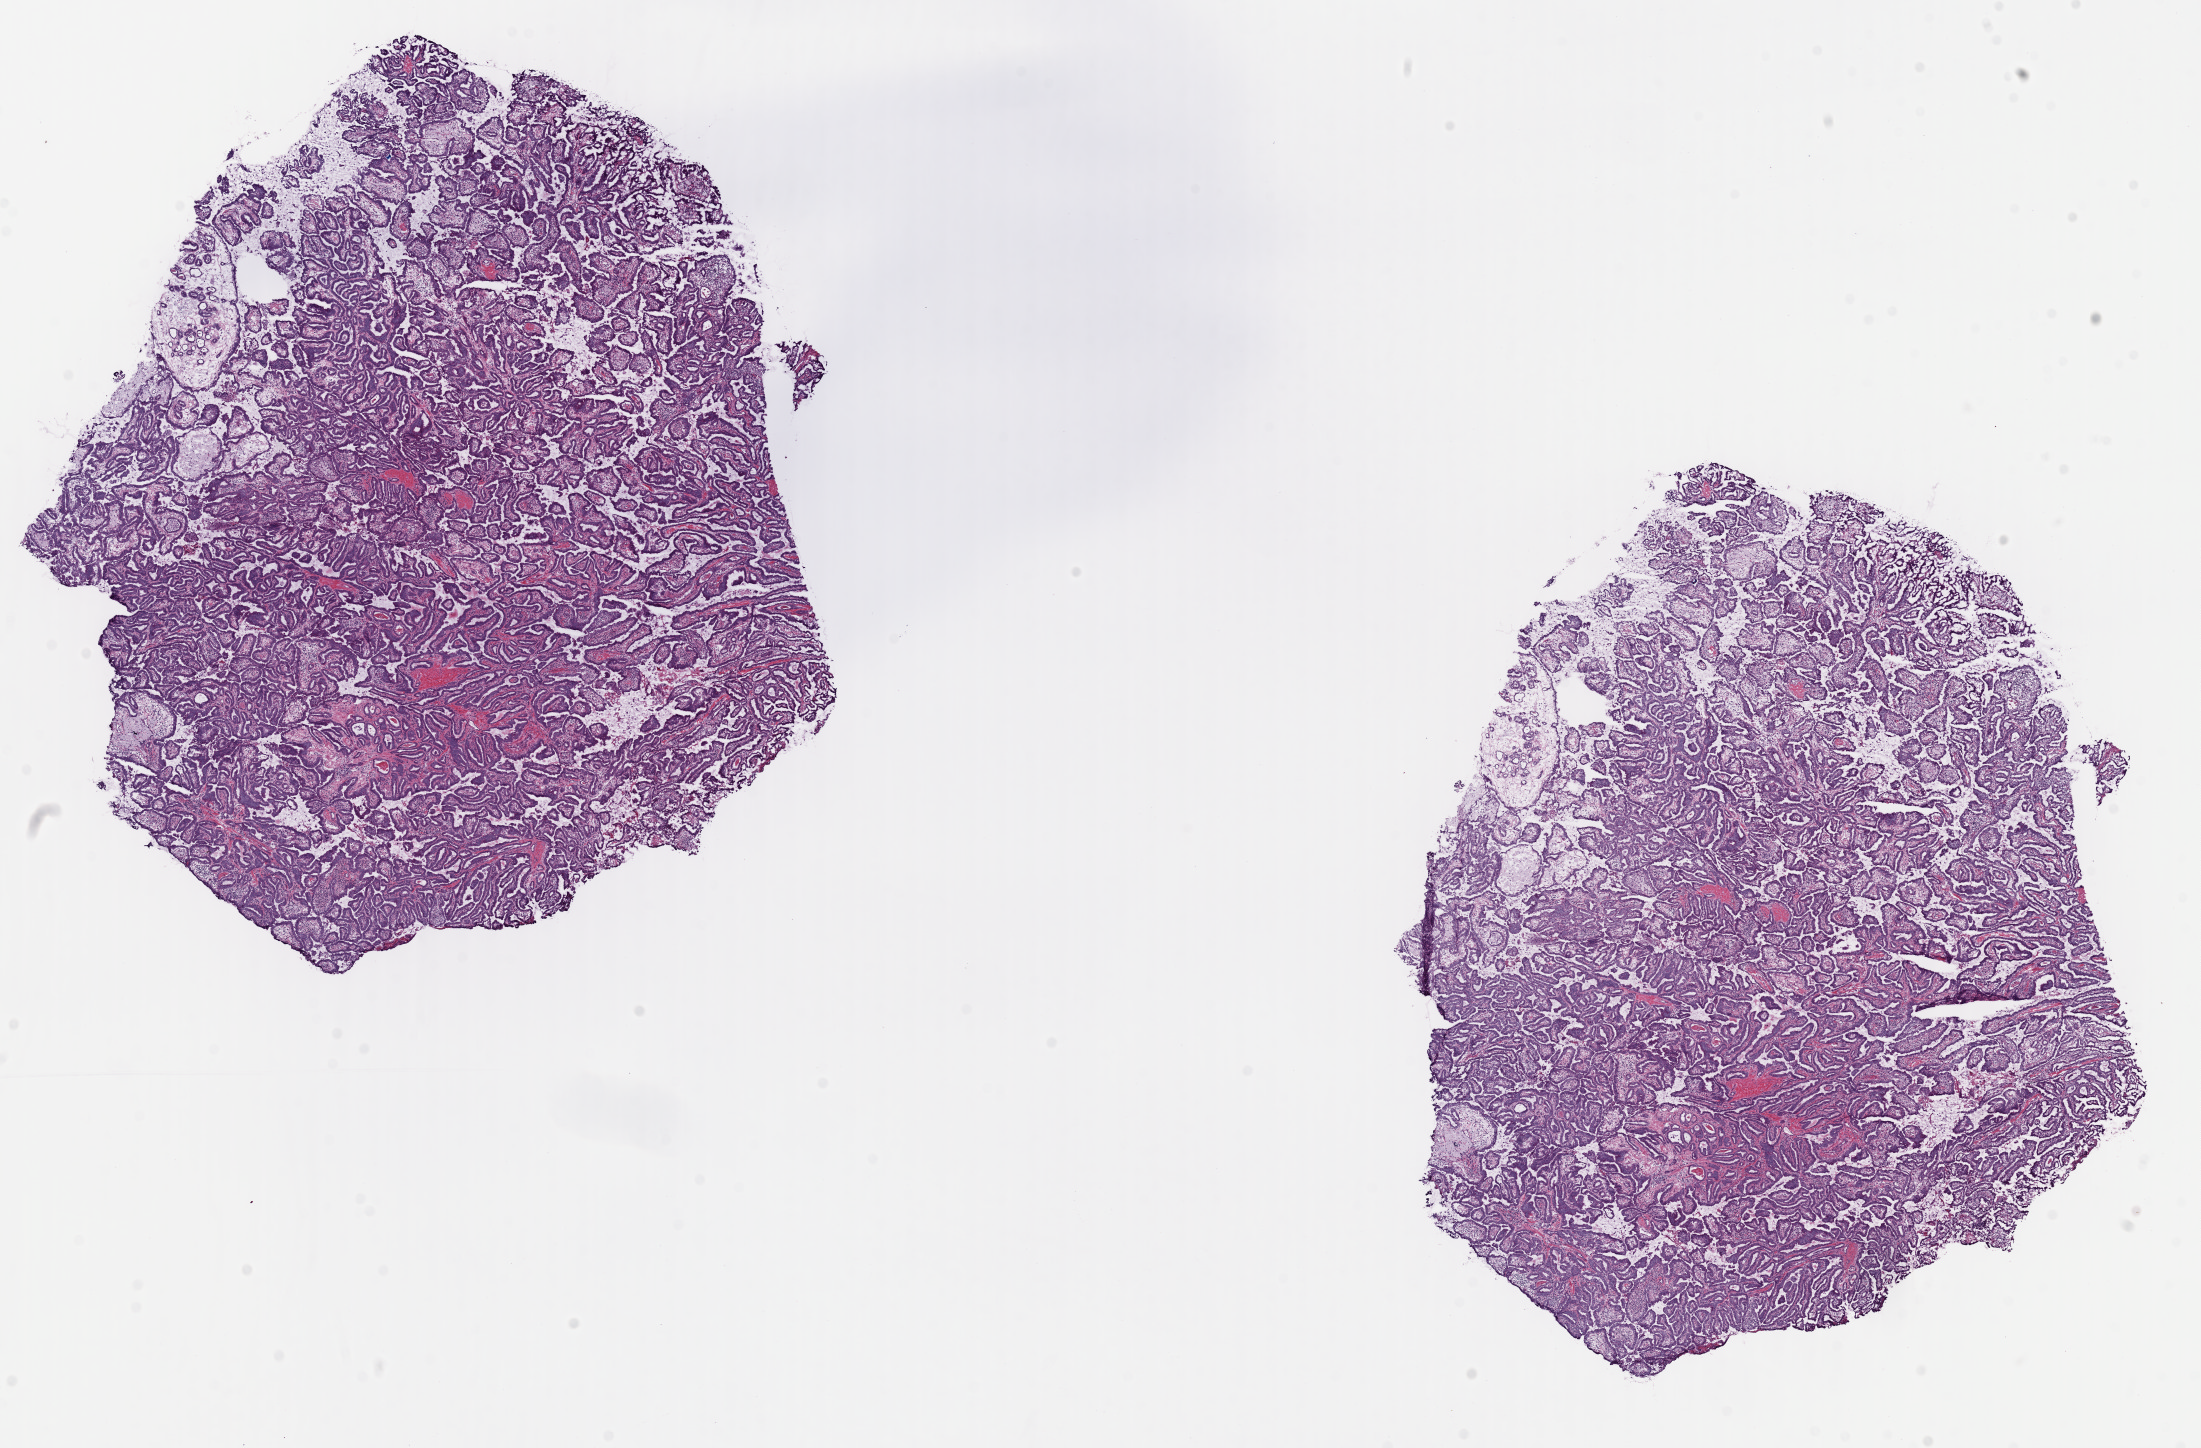
Whole-slide histology image, Hematoxylin and eosin (H&E) stained, whole scanned area (about 17.4 x 11.4 mm, from a 40x scan) shown as a low-resolution overview. Frozen section from the top of the tissue portion. Thyroid, primary tumour sample. Patient: female, age at initial diagnosis 26 years. Slide review estimates, as recorded: tumour cells 100%, tumour nuclei 85%, normal cells 0%, stromal cells 0%, necrosis 0%. Infiltration values recorded for this section: lymphocyte infiltration 0%, monocyte infiltration 0%, neutrophil infiltration 0%.
Laterality: right. Lymph nodes positive (case pathology): 2 of 2 examined. AJCC pathologic stage: I (6th edition). Histologic diagnosis: Papillary adenocarcinoma, NOS (thyroid gland).